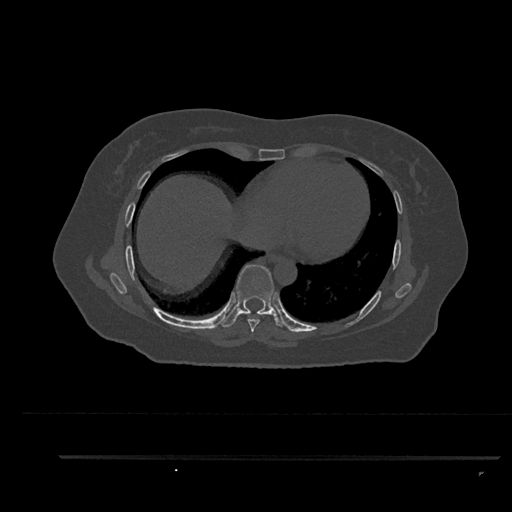
CT including the spine, one axial slice; position 479 of 797 along the scan axis; reconstruction kernel Br40s/3; 120 kVp; bone window (W 1800 / L 400 HU); 0.5 mm slice thickness; 512 × 512 image matrix. Patient: female, 44 years. Case-level facts recorded for this patient, not image findings: primary cancer: renal.
Annotated regions visible in this slice (semi-automatically segmented with operator editing):
- T7 vertebra: box from (x=243, y=313) to (x=260, y=332) px
- T8 vertebra: (x=222, y=264)–(x=285, y=328)